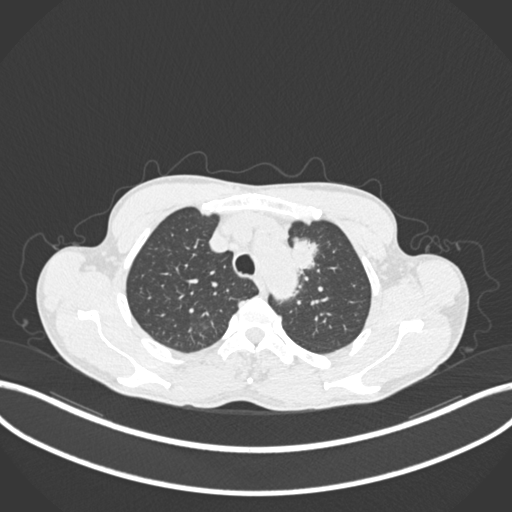
Chest CT, one axial slice; position 162 of 211 along the scan axis; reconstruction kernel B30f; 120 kVp; lung window (W 1500 / L -600 HU); 512 × 512 image matrix, field of view 400 × 400 mm. Patient: male, 58 years. Case-level facts recorded for this patient, not image findings: clinical TNM (as recorded): T1c N1 M0.
Outlined on this slice (bounding box drawn by a radiologist):
- lung tumour (recorded histology: adenocarcinoma): bounding box [x1, y1, x2, y2] px = [289, 231, 322, 274]